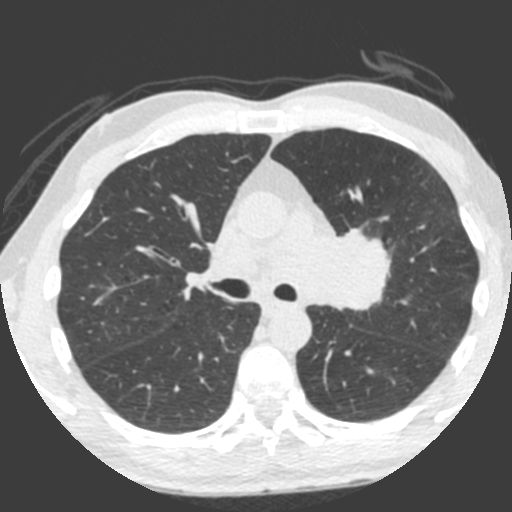
Low-dose screening chest CT, one axial slice; slice 138 of 212 in the series (ordered by position); lung window (W 1500 / L -600 HU); 2 mm slice thickness; 512 × 512 image matrix, field of view 315 × 315 mm.
Structures marked on this image (outlined manually by an expert reader):
- lesion 1 (tumor, upper lobe of left lung): bounding box [x1, y1, x2, y2] px = [318, 227, 390, 311]